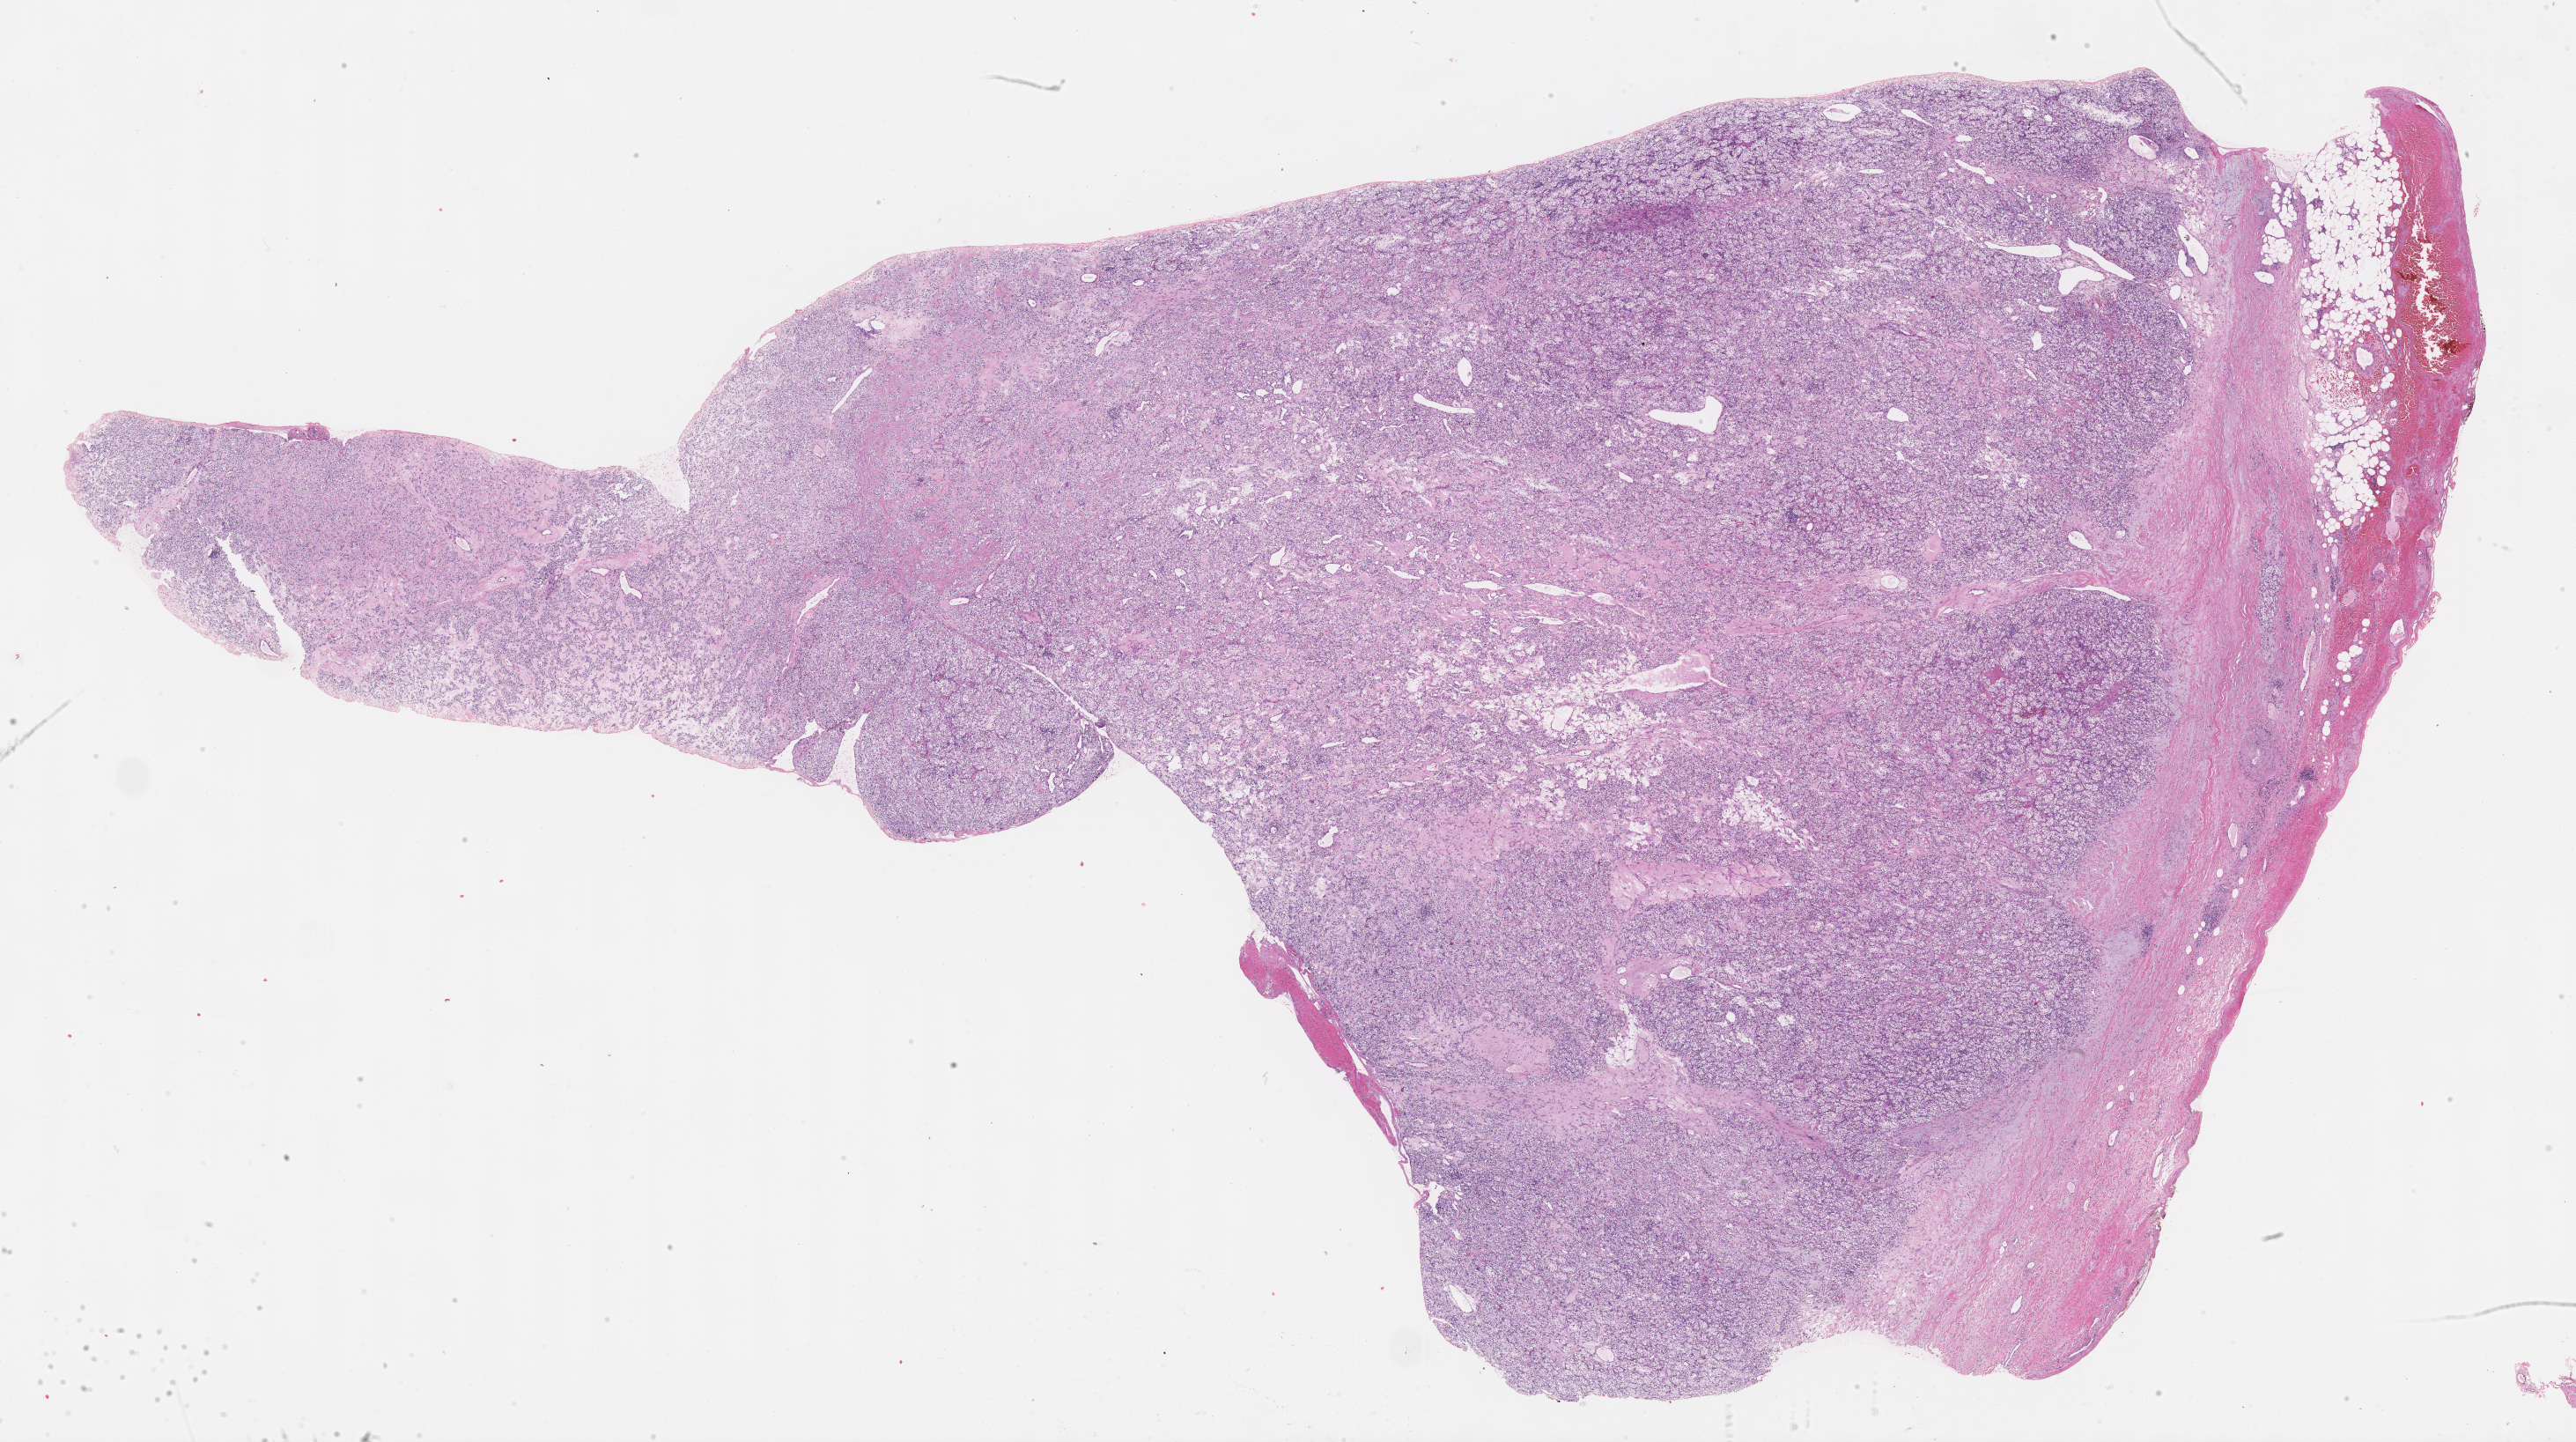
Whole-slide histology image, H&E, whole scanned area (about 23.6 x 13.2 mm, from a 40x scan) shown as a low-resolution overview. FFPE section. Sample: primary tumour, kidney. Female patient; age at initial diagnosis 52 years. Histologic grade: G4 (undifferentiated).
AJCC pathologic stage: IV. Diagnosis: Clear cell adenocarcinoma, NOS.